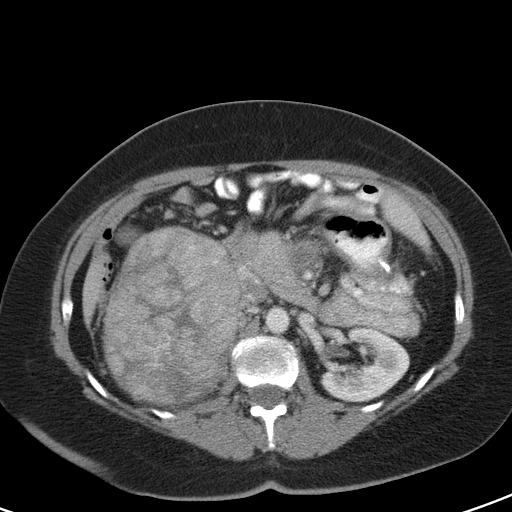
Contrast-enhanced abdominal CT, one axial slice. 120 kVp. Intravenous contrast given. Soft-tissue window (W 400 / L 40 HU). 5 mm slice thickness. 512 × 512 image matrix, field of view 356 × 356 mm. Female patient, age 51 years. From the clinical record (not read from this slice): diagnosis: adrenocortical carcinoma; tumour side: right adrenal; tumour size at pathology: 17 cm; Ki-67 index: 12 %; stage (as recorded): 2.
Annotated regions visible in this slice (semi-automatic segmentation, software-assisted and operator-edited):
- mass: bounding box (x1, y1, x2, y2) in pixels: (104, 227, 238, 404)